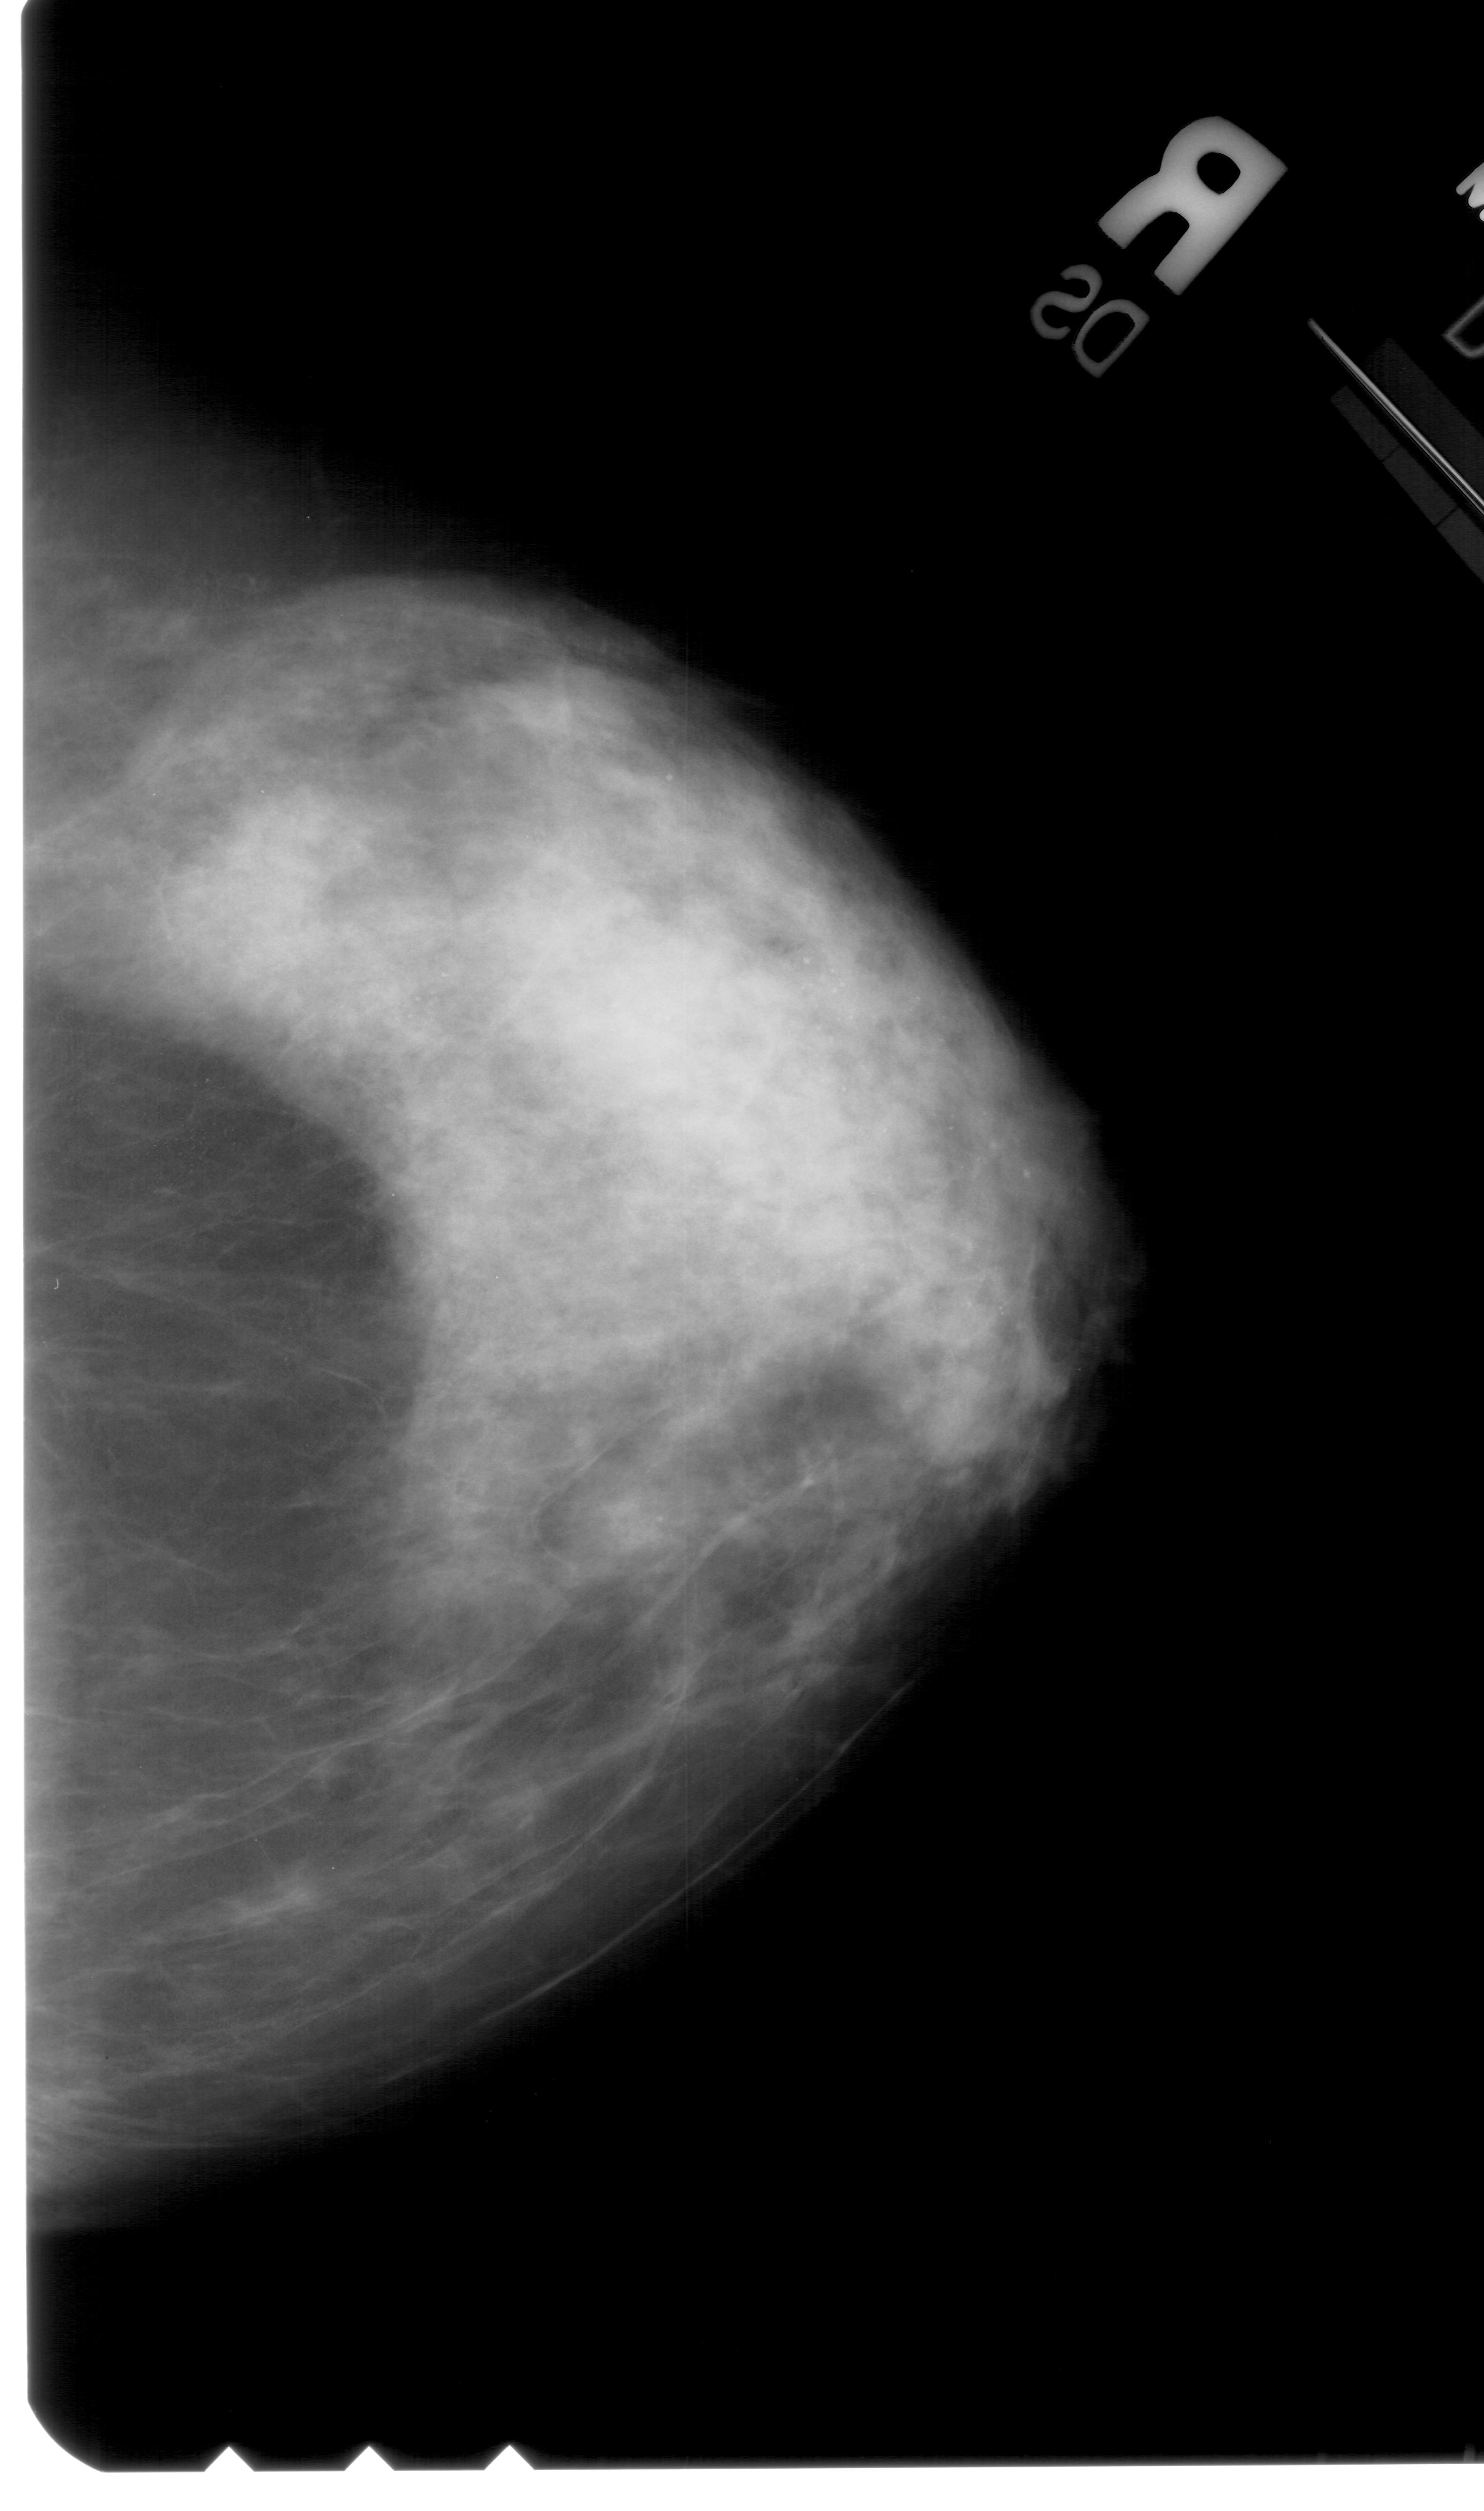
Scanned film-screen mammogram; right breast; craniocaudal (CC) view; BI-RADS breast density category 4 (scale 1–4).
Marked abnormality: calcifications, morphology amorphous, distribution segmental; BI-RADS assessment category 4; subtlety rating 3 on a 1 (subtle) to 5 (obvious) scale; pathology result (as recorded, not read from the image): benign.